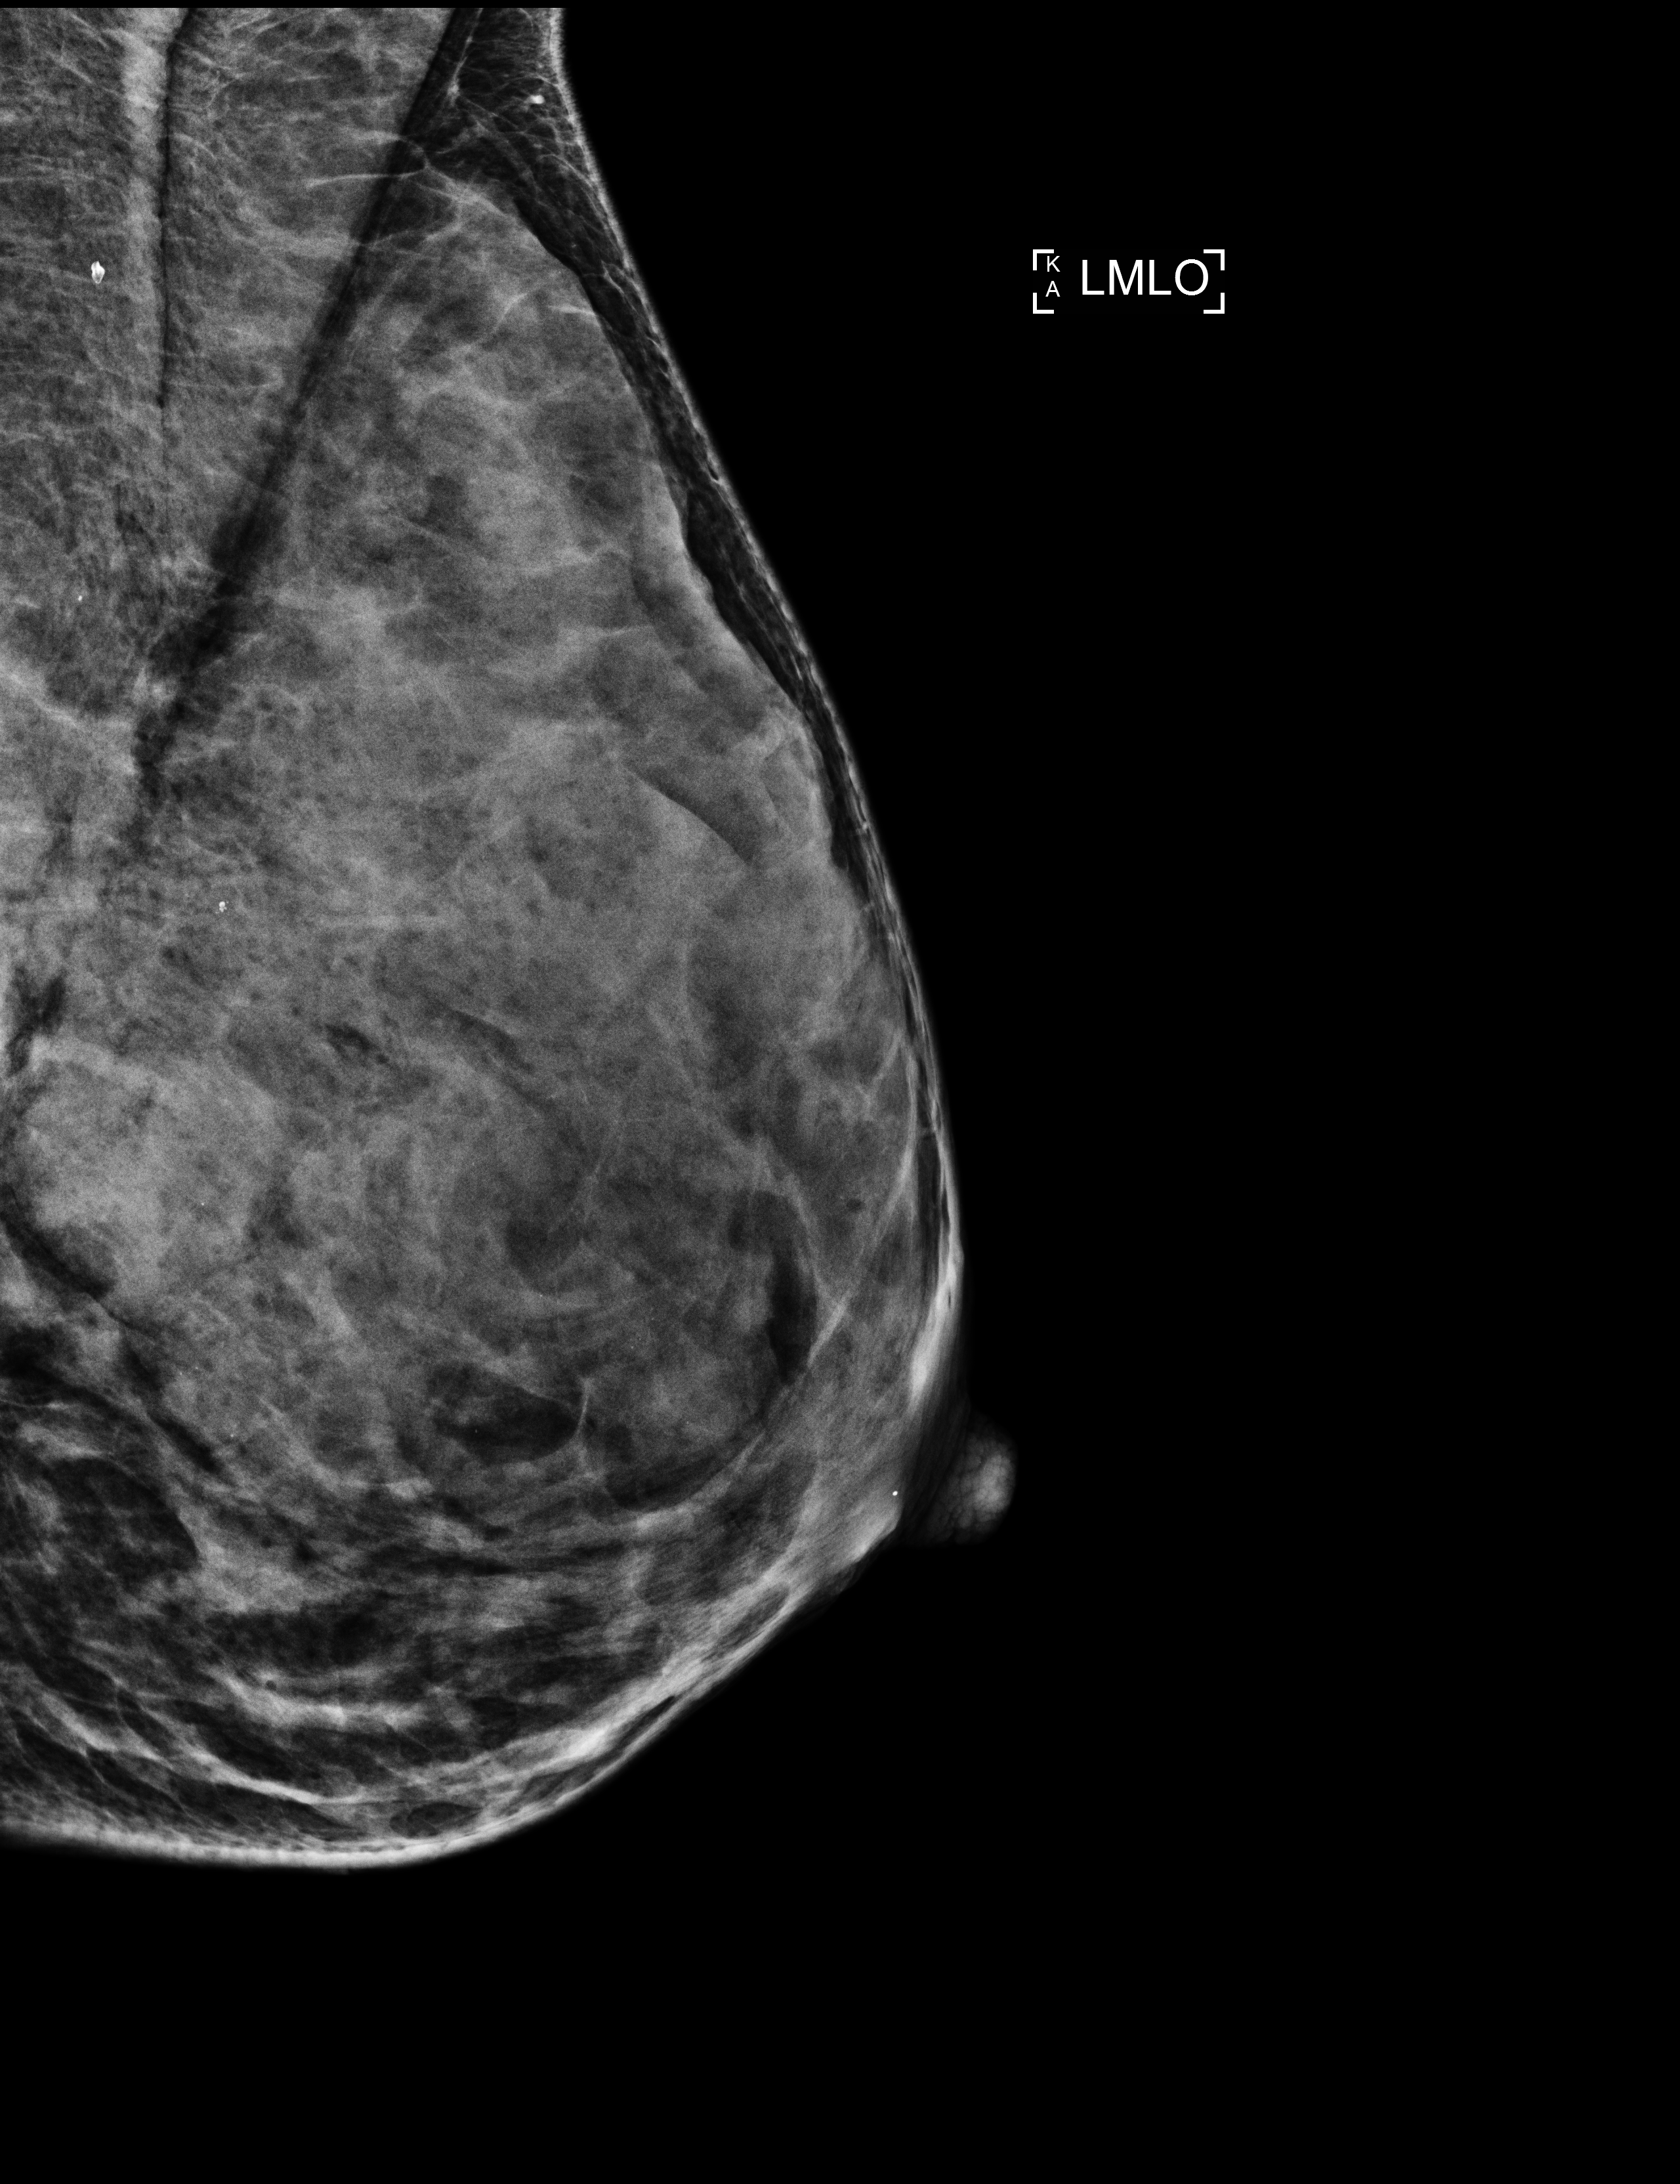
Full-field digital mammogram (FFDM), left breast, MLO view, annual screening mammography examination, system: Selenia Dimensions. Patient: female, 41 years.
Breast density at the screening exam (both breasts): extremely dense (BI-RADS density category d). Final BI-RADS assessment for this screening round (tomosynthesis exam, both breasts): category 2. Recall: no recall after this screen.